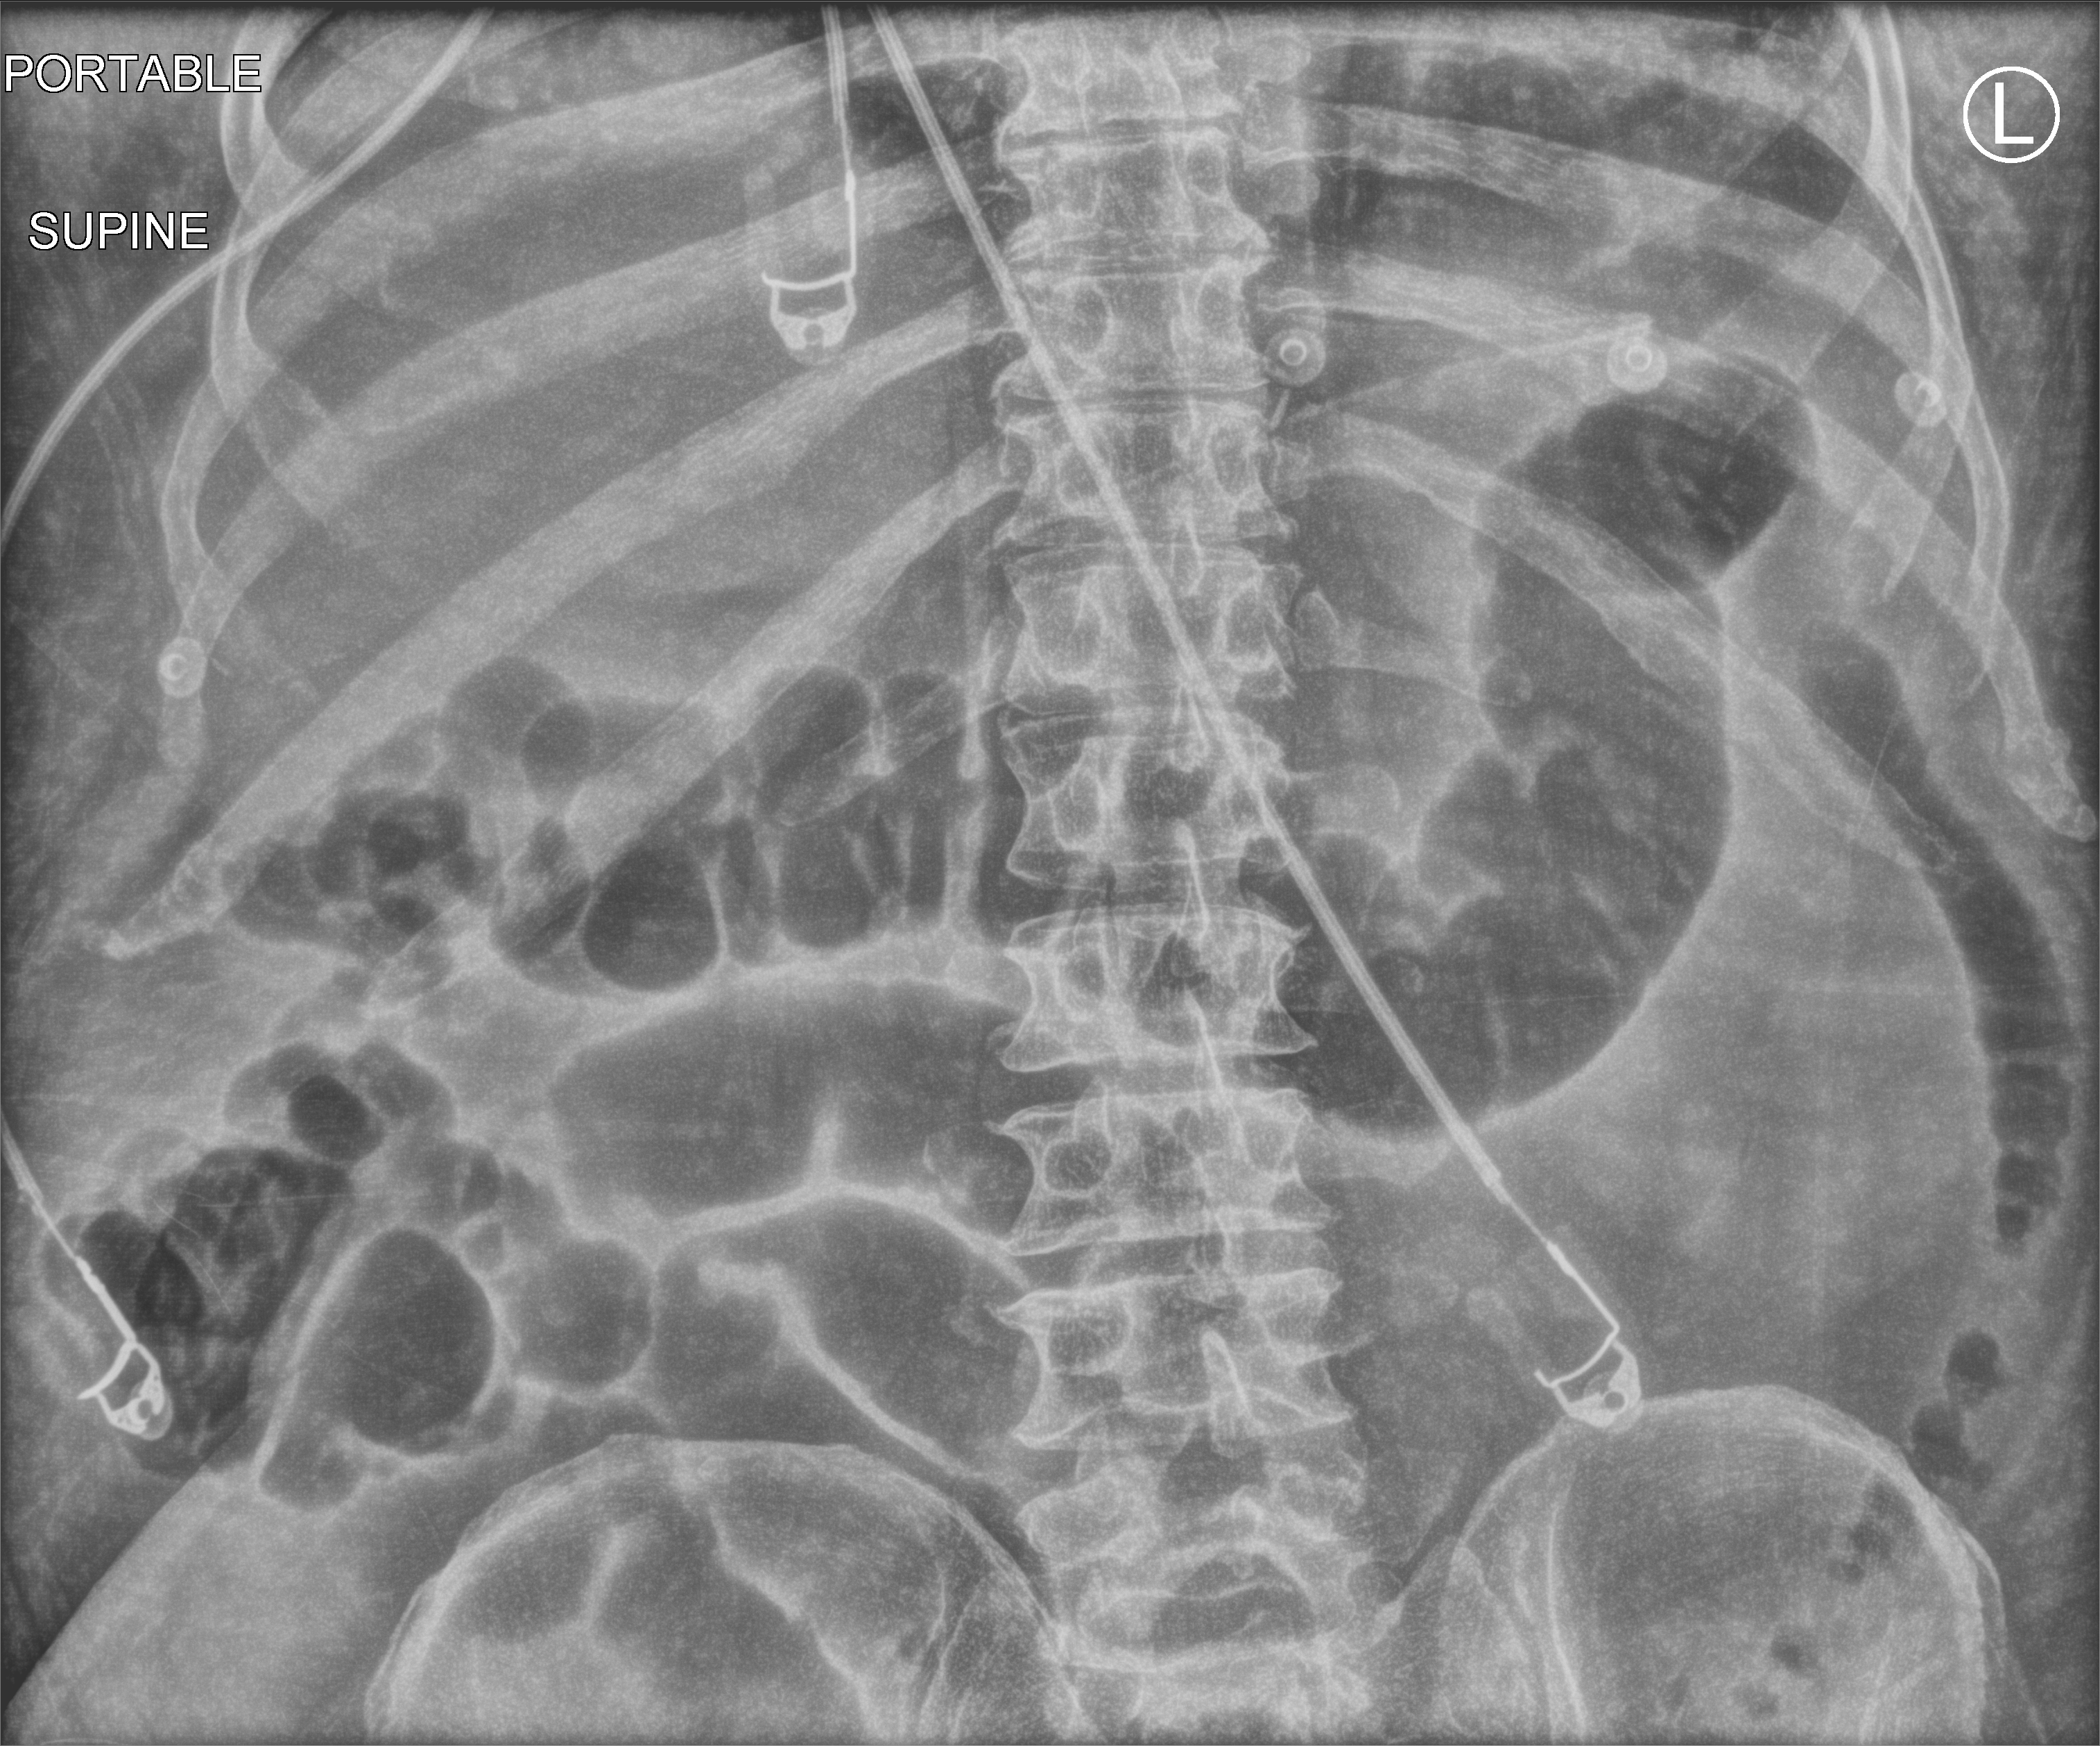
Portable abdomen radiograph; anteroposterior (AP) projection. Patient hospitalised with COVID-19; male, aged 18–59 years.
Hospital-stay facts (about this admission, not read from this image; timing relative to this image not recorded):
- mechanically ventilated during this hospital stay: yes
- COPD (admission record): no